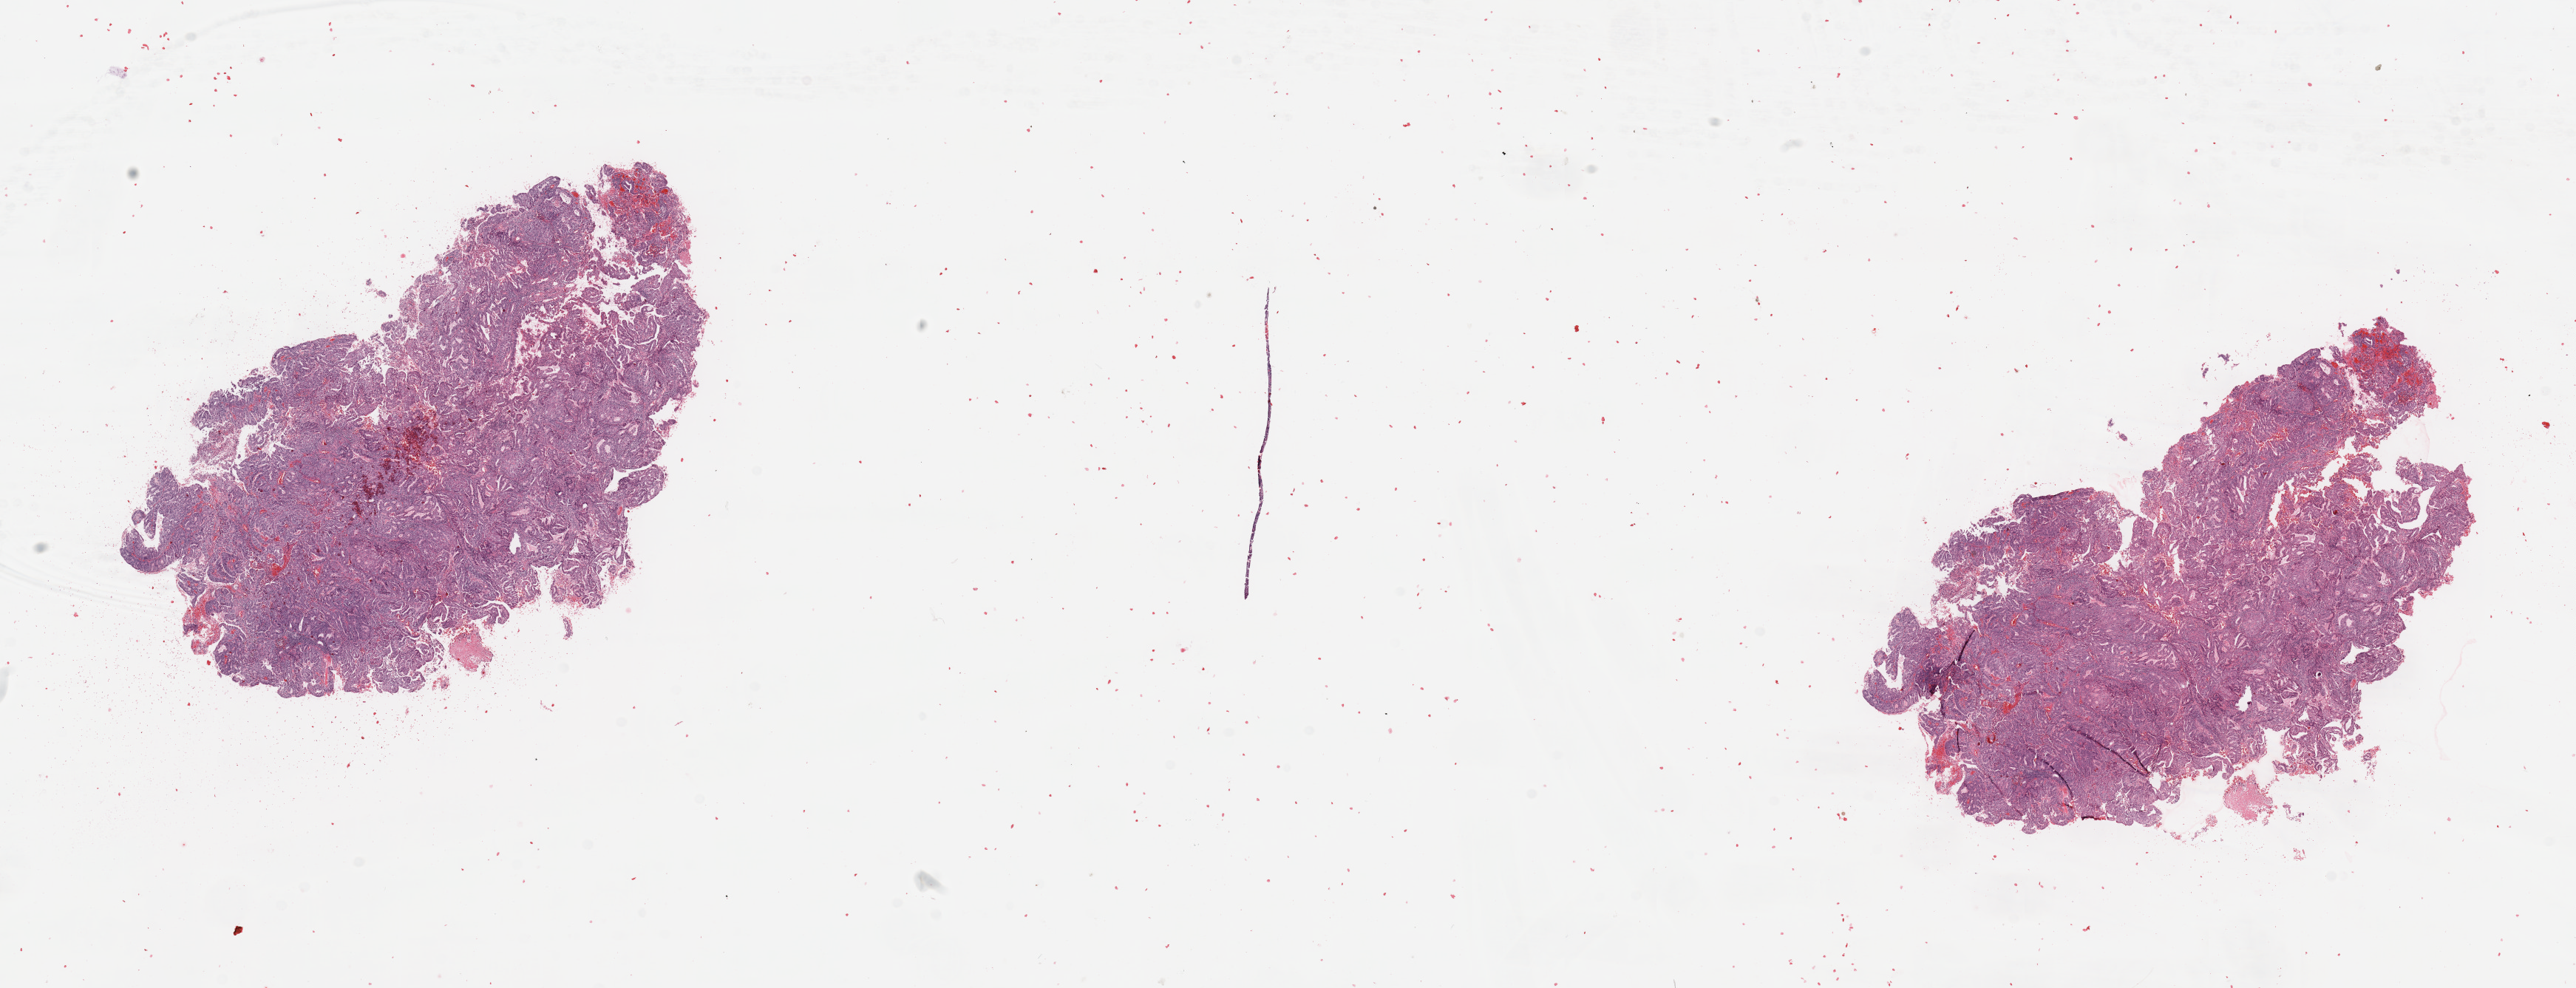
Whole-slide histology image, H&E-stained, a low-resolution overview of the entire scanned area, about 27.6 x 10.6 mm; tumour tissue sample, sampled site: uterus. Female, 51 y/o. Histologic grade: G2 (moderately differentiated). Slide review estimates, as recorded: tumour nuclei 90%, necrosis 2%.
AJCC pathologic stage: I. Diagnosis: Endometrioid adenocarcinoma, NOS.